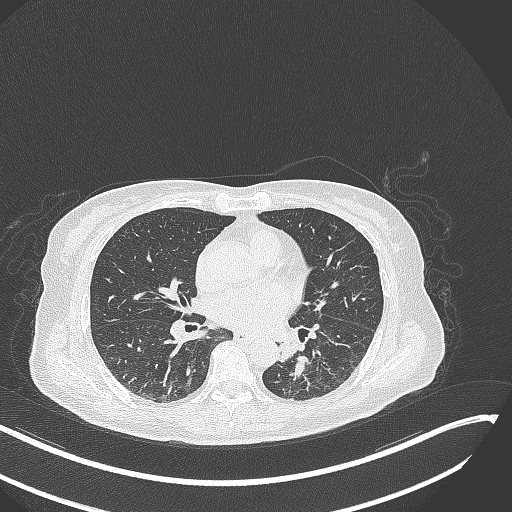
Chest CT, one axial slice. Position 127 of 342 along the scan axis. Reconstruction kernel B70f. 120 kVp. Lung window (W 1500 / L -600 HU). 1 mm slice thickness. 512 × 512 image matrix, field of view 400 × 400 mm. Female patient, age 64 years. From the clinical record (not read from this slice): clinical TNM (as recorded): T3 N1 M1.
Outlined on this slice (rectangle marked by the reading radiologist):
- lung tumour (recorded histology: small cell carcinoma): bounding box <272,337,313,380> (left, top, right, bottom; pixels)